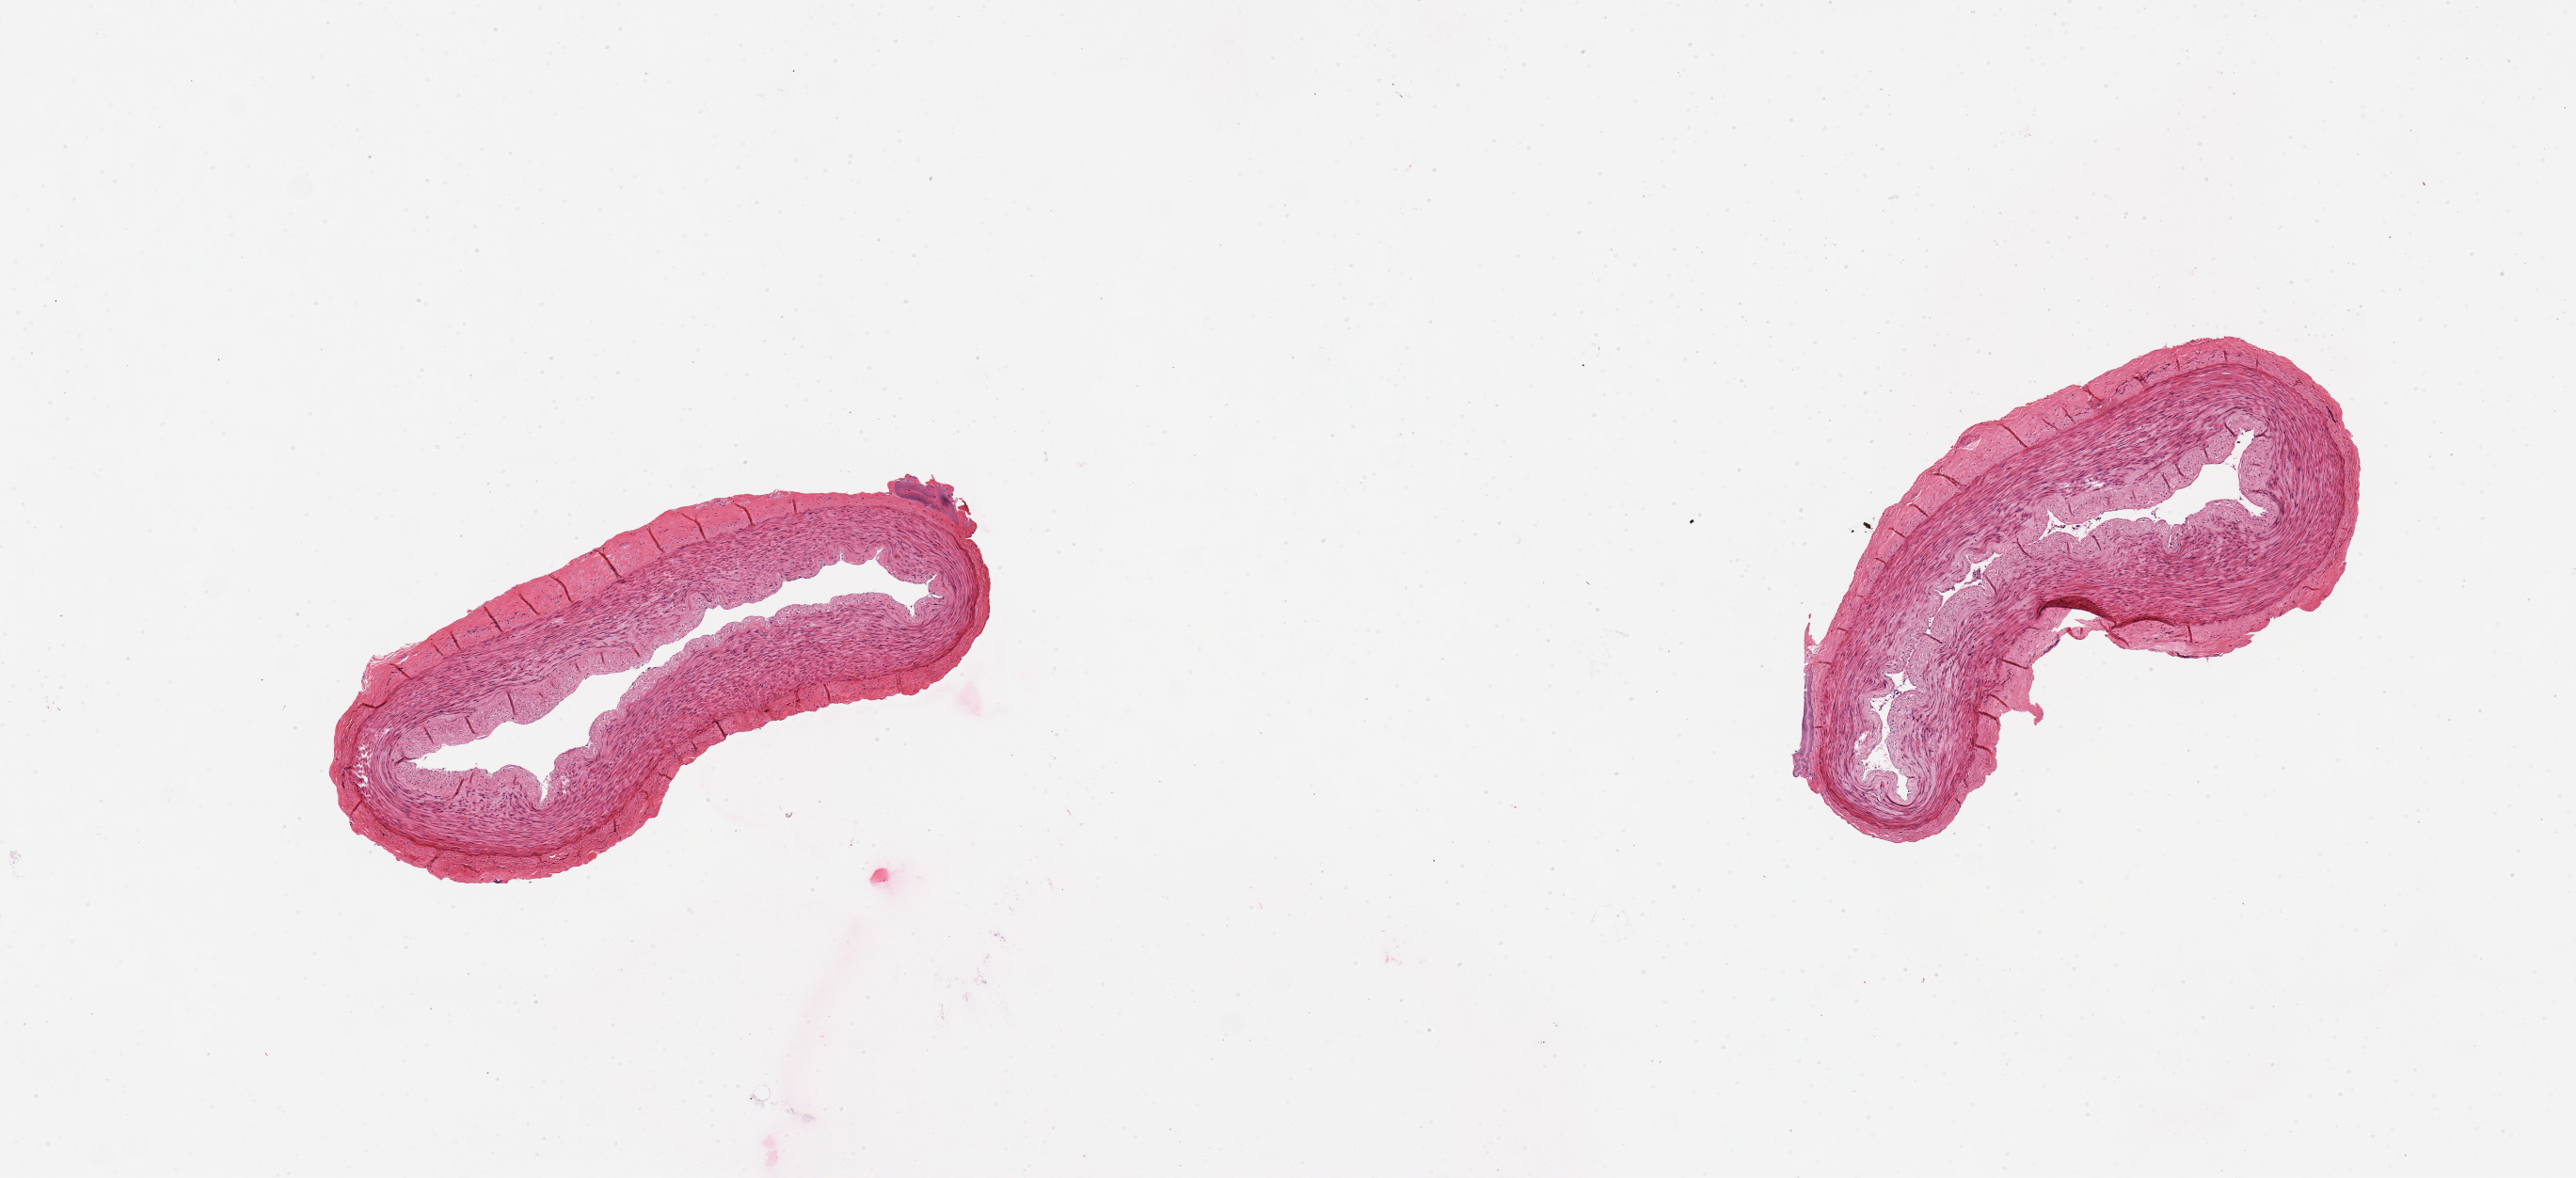
Digitized H&E-stained section — low-resolution overview of the scanned area, about 10.8 x 5.0 mm; PAXgene-fixed paraffin-embedded (PFPE) section; sampled site (target tissue): tibial artery; donor tissue sample. Donor sex: male.
* pathologist's review note for this sample: 2 pieces; no fat; no sclerosis